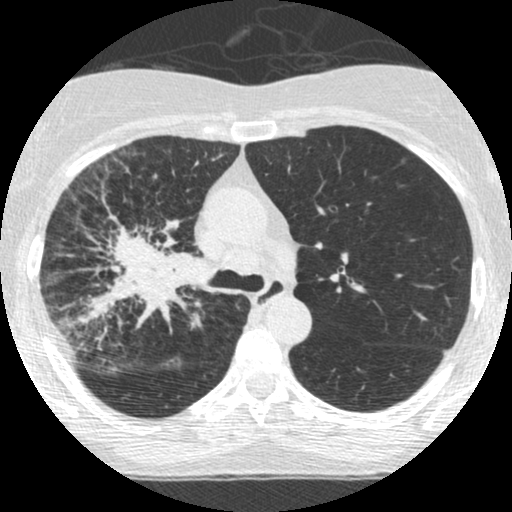
Low-dose screening chest CT, one axial slice. Lung window (W 1500 / L -600 HU). 1.25 mm slice thickness. 512 × 512 image matrix, field of view 294 × 294 mm.
Annotated regions visible in this slice (outlined manually by an expert reader):
- lesion 2 (tumor, hilum of right lung): bounding box <86,219,206,322> (left, top, right, bottom; pixels)